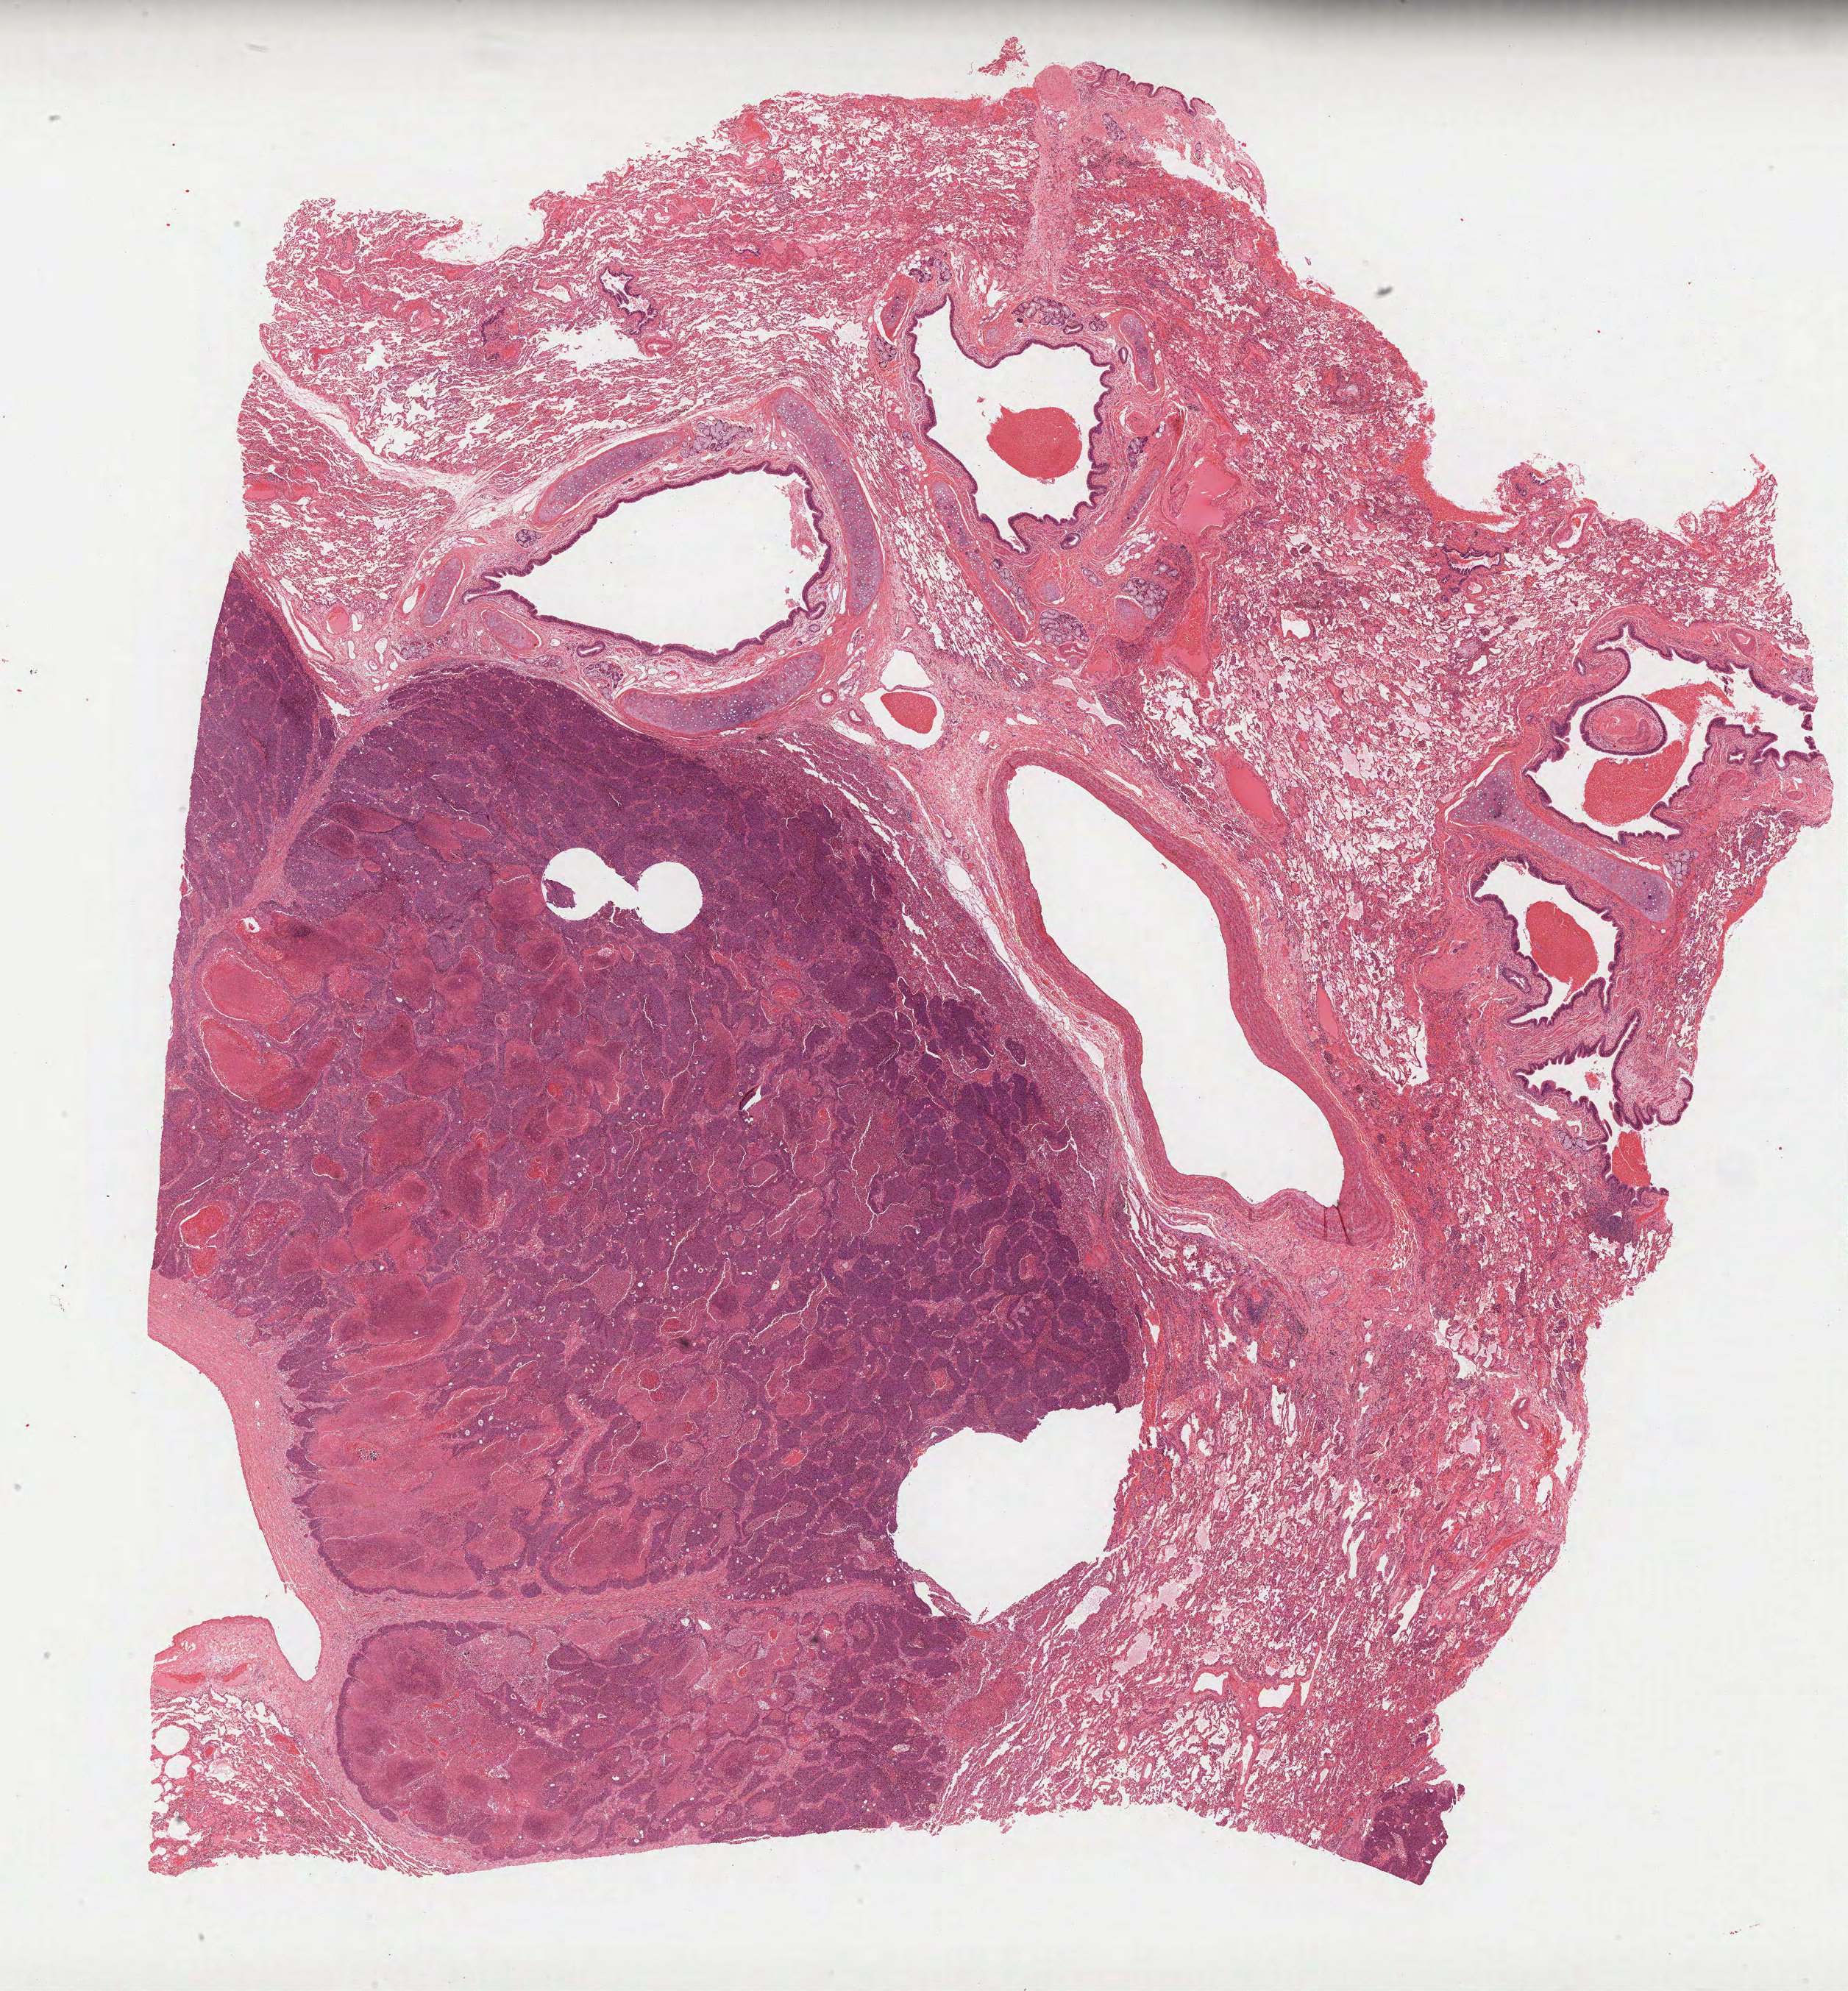
H&E whole-slide image, low-resolution overview of the scanned area, about 20.3 x 21.8 mm (from a 40x scan), formalin-fixed paraffin-embedded (FFPE) diagnostic section, primary tumour sample from the lung. Male, age 50 years at initial diagnosis.
Histologic diagnosis: Squamous cell carcinoma, NOS (lower lobe, lung). AJCC pathologic stage: IB.